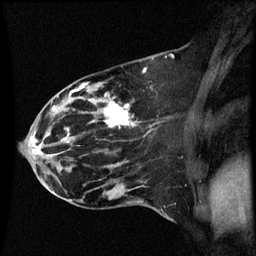
Breast MRI (dynamic contrast-enhanced), one sagittal slice. Slice 24 of 60 in the series (ordered by position). Dynamic contrast-enhanced series, image 2 of 3 at this slice position (ordered by acquisition). 1.5 T. TE 4.2 ms, TR 8.9 ms. 2 mm slice thickness. 256 × 256 image matrix, field of view 200 × 200 mm. Patient: female, 44 years. Case-level facts recorded for this patient, not image findings: setting: breast cancer imaged before/during neoadjuvant chemotherapy; receptor status: HR-positive, HER2-negative.
Structures marked on this image (semi-automatically segmented with operator editing):
- analysis volume of interest (the breast-tissue region the enhancement analysis was run in; not a lesion): box from (x=43, y=78) to (x=147, y=189) px
- tumour enhancement mask (voxels above the 70 % enhancement threshold inside the analysis volume of interest): (x=62, y=86)–(x=131, y=141)